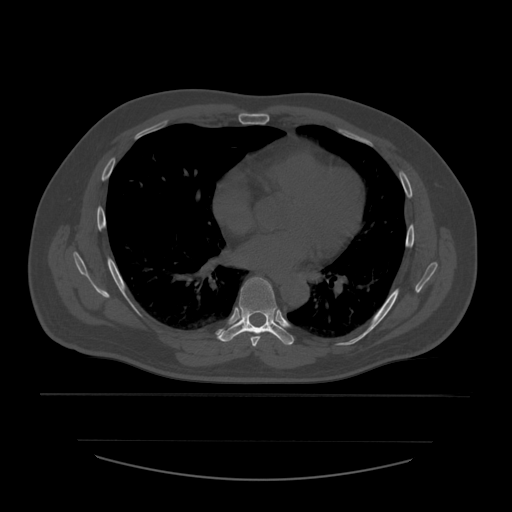
CT including the spine, one axial slice; slice 364 of 532 in the series (ordered by position); reconstruction kernel STANDARD; 120 kVp; bone window (W 1800 / L 400 HU); 1.25 mm slice thickness; 512 × 512 image matrix. Patient age 44 years. From the clinical record (not read from this slice): primary cancer: soft tissue sarcoma.
Annotated regions visible in this slice (semi-automatic segmentation, software-assisted and operator-edited):
- T6 vertebra: box from (x=250, y=333) to (x=262, y=347) px
- T7 vertebra: (x=217, y=278)–(x=294, y=346)